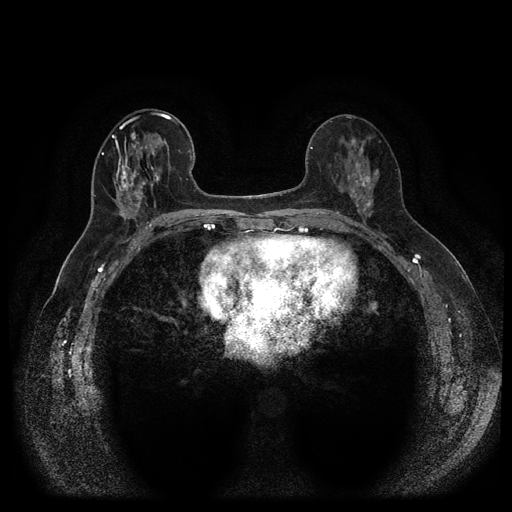
Breast MRI (dynamic contrast-enhanced, multi-phase), one axial slice; slice 46 of 116 in the series (ordered by position); dynamic contrast-enhanced series, time point 2 of 5 at this slice position (early post-contrast); 1.5 T; TE 2.6 ms, TR 5.4 ms; 2 mm slice thickness; 512 × 512 image matrix. Female patient, age 56 years.
Structures marked on this image (semi-automatic segmentation, software-assisted and operator-edited):
- breast lesion (labelled 'tumour' in the annotation; benign lesions carry a separate 'benign' label): bounding box <112,155,138,196> (left, top, right, bottom; pixels)